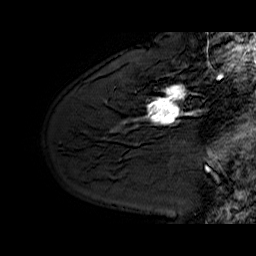
Breast MRI (dynamic contrast-enhanced), one sagittal slice. Slice 45 of 60 in the series (ordered by position). Dynamic contrast-enhanced series, time point 2 of 6 at this slice position (early post-contrast). 1.5 T. TE 6.4 ms, TR 32.9 ms. 4 mm slice thickness. 256 × 256 image matrix, field of view 200 × 200 mm. Female patient. From the clinical record (not read from this slice): setting: breast cancer imaged before/during neoadjuvant chemotherapy; receptor status: HER2-positive.
Outlined on this slice (semi-automatic segmentation, software-assisted and operator-edited):
- analysis volume of interest (the breast-tissue region the enhancement analysis was run in; not a lesion): bounding box [x1, y1, x2, y2] px = [130, 62, 210, 128]
- tumour enhancement mask (voxels above the 100 % enhancement threshold inside the analysis volume of interest): [147, 85, 199, 124]